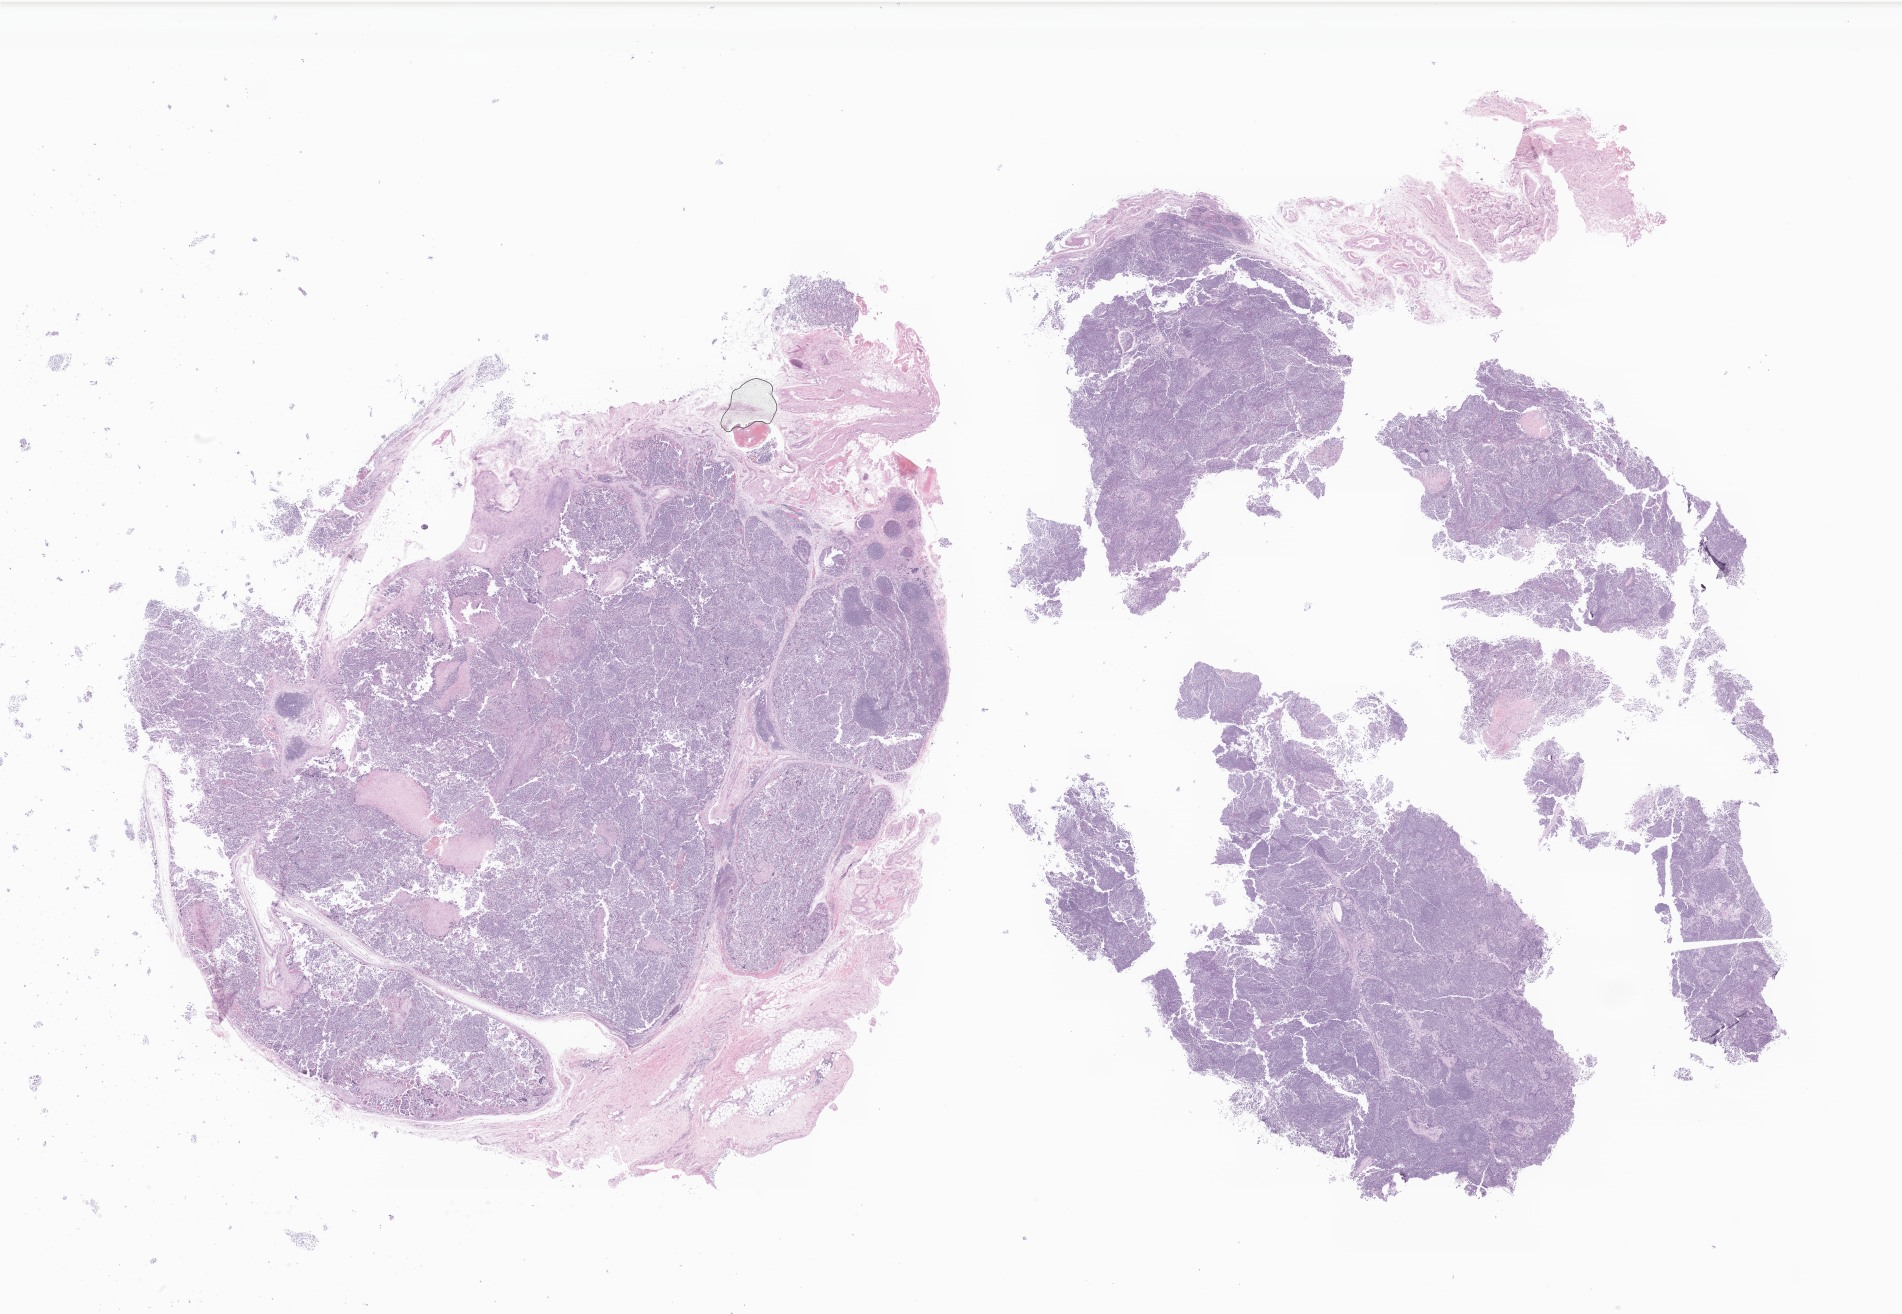
Digitized haematoxylin and eosin-stained section of tumor tissue from the retroperitoneum — a low-resolution overview of the entire scanned area, about 32.1 x 22.2 mm. Formalin-fixed paraffin-embedded section. Patient: female, age 63 months (5 years 3 months).
* recorded diagnosis: Neuroblastoma, NOS